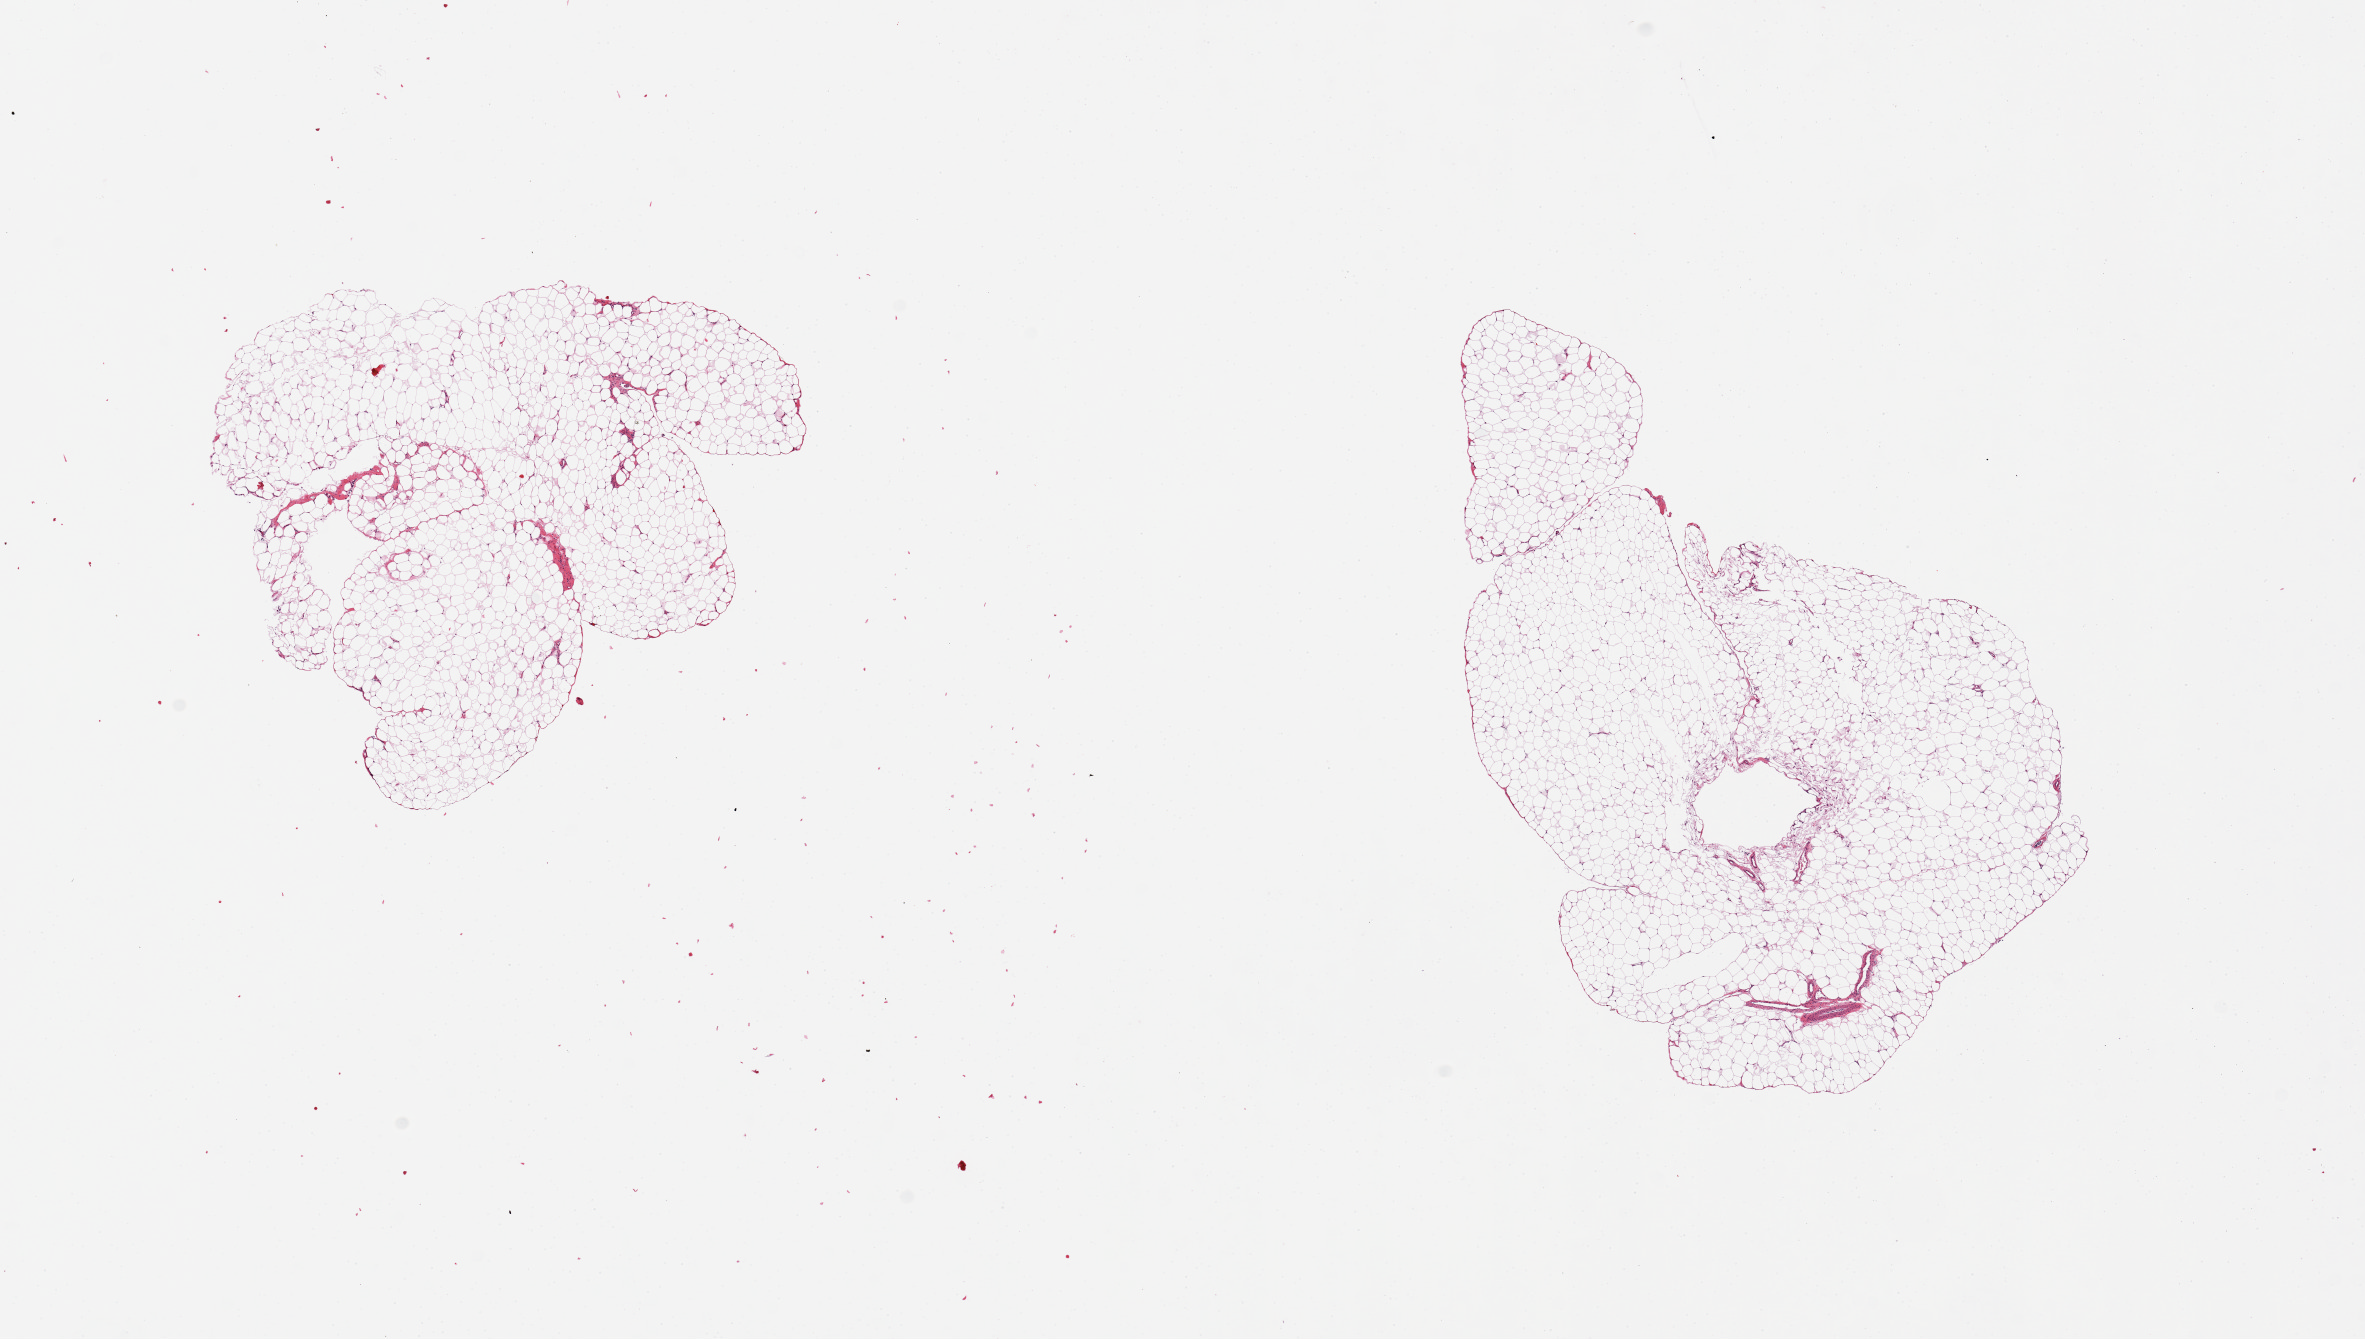
H&E whole-slide image, whole scanned area (about 18.7 x 10.6 mm, slide scanned at 20x) shown as a low-resolution overview, PAXgene-fixed paraffin-embedded (PFPE) section, target tissue: omentum, tissue donor sample. Female donor.
Review note (as recorded): 2 pieces.